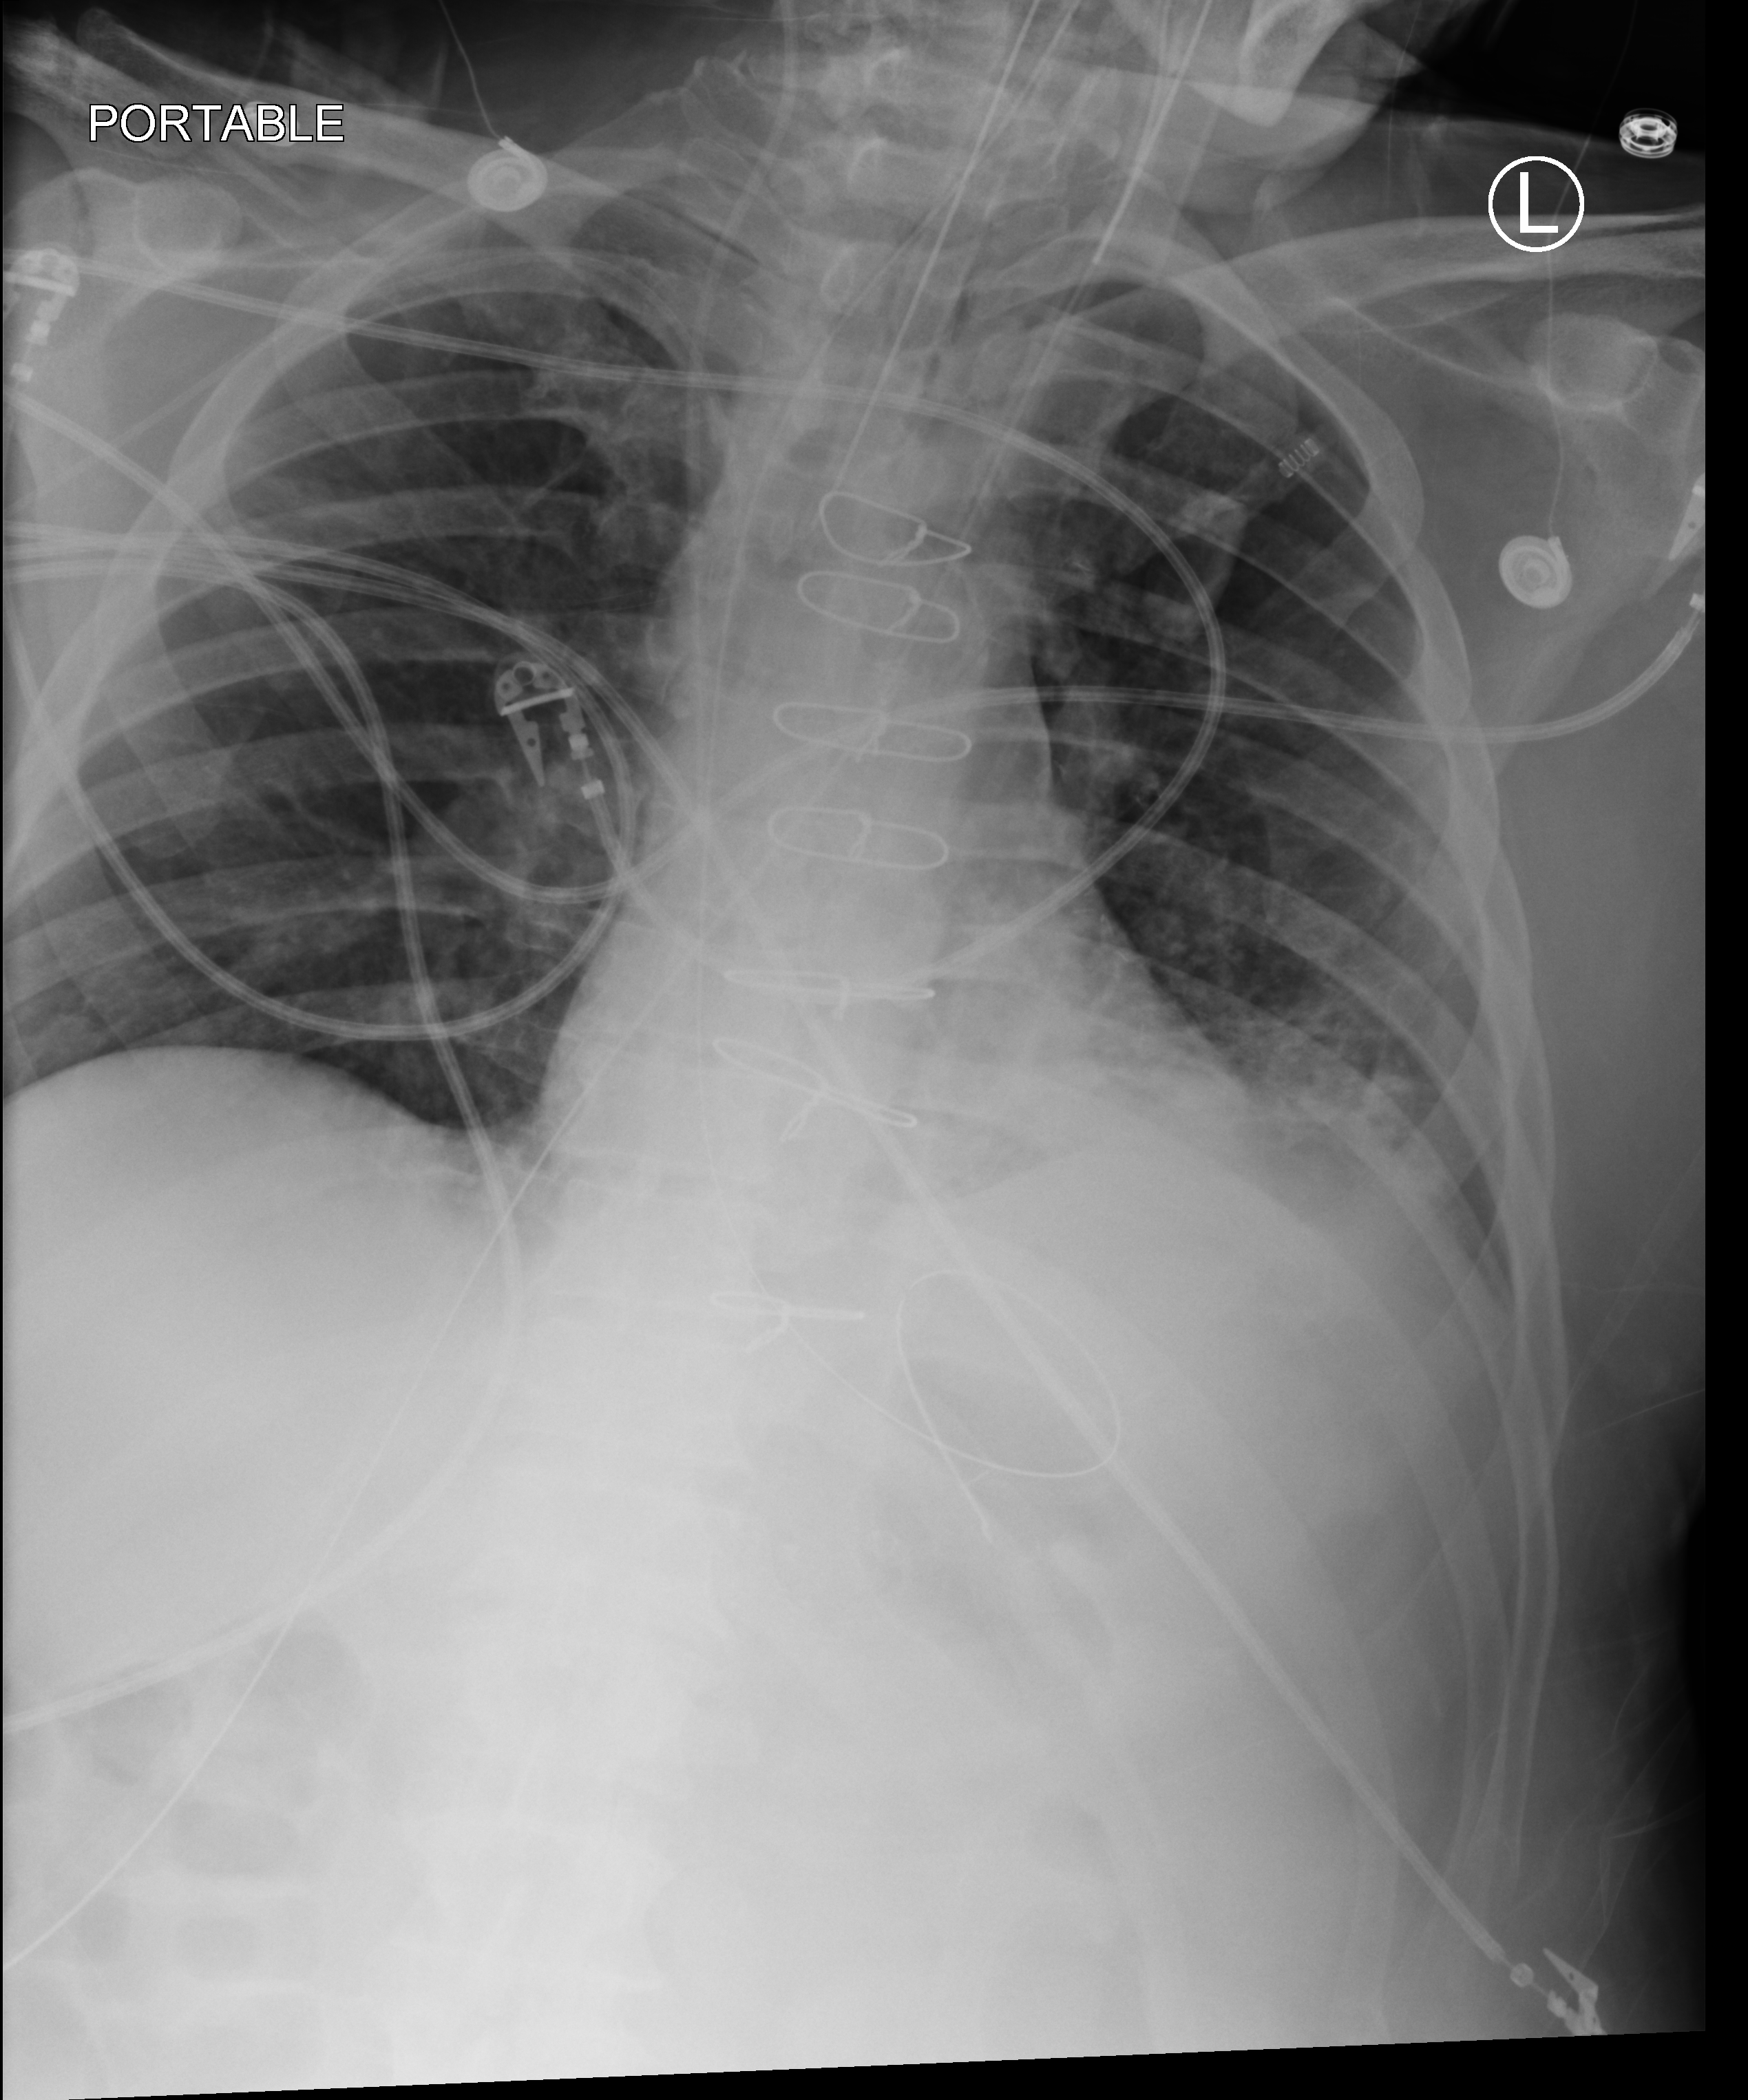
Chest X-ray (portable); anteroposterior (AP) projection. Patient hospitalised with COVID-19; male, aged 60–74 years.
Admission-level facts for this patient (not findings on this image; timing relative to this image not recorded): mechanically ventilated during this hospital stay: yes.